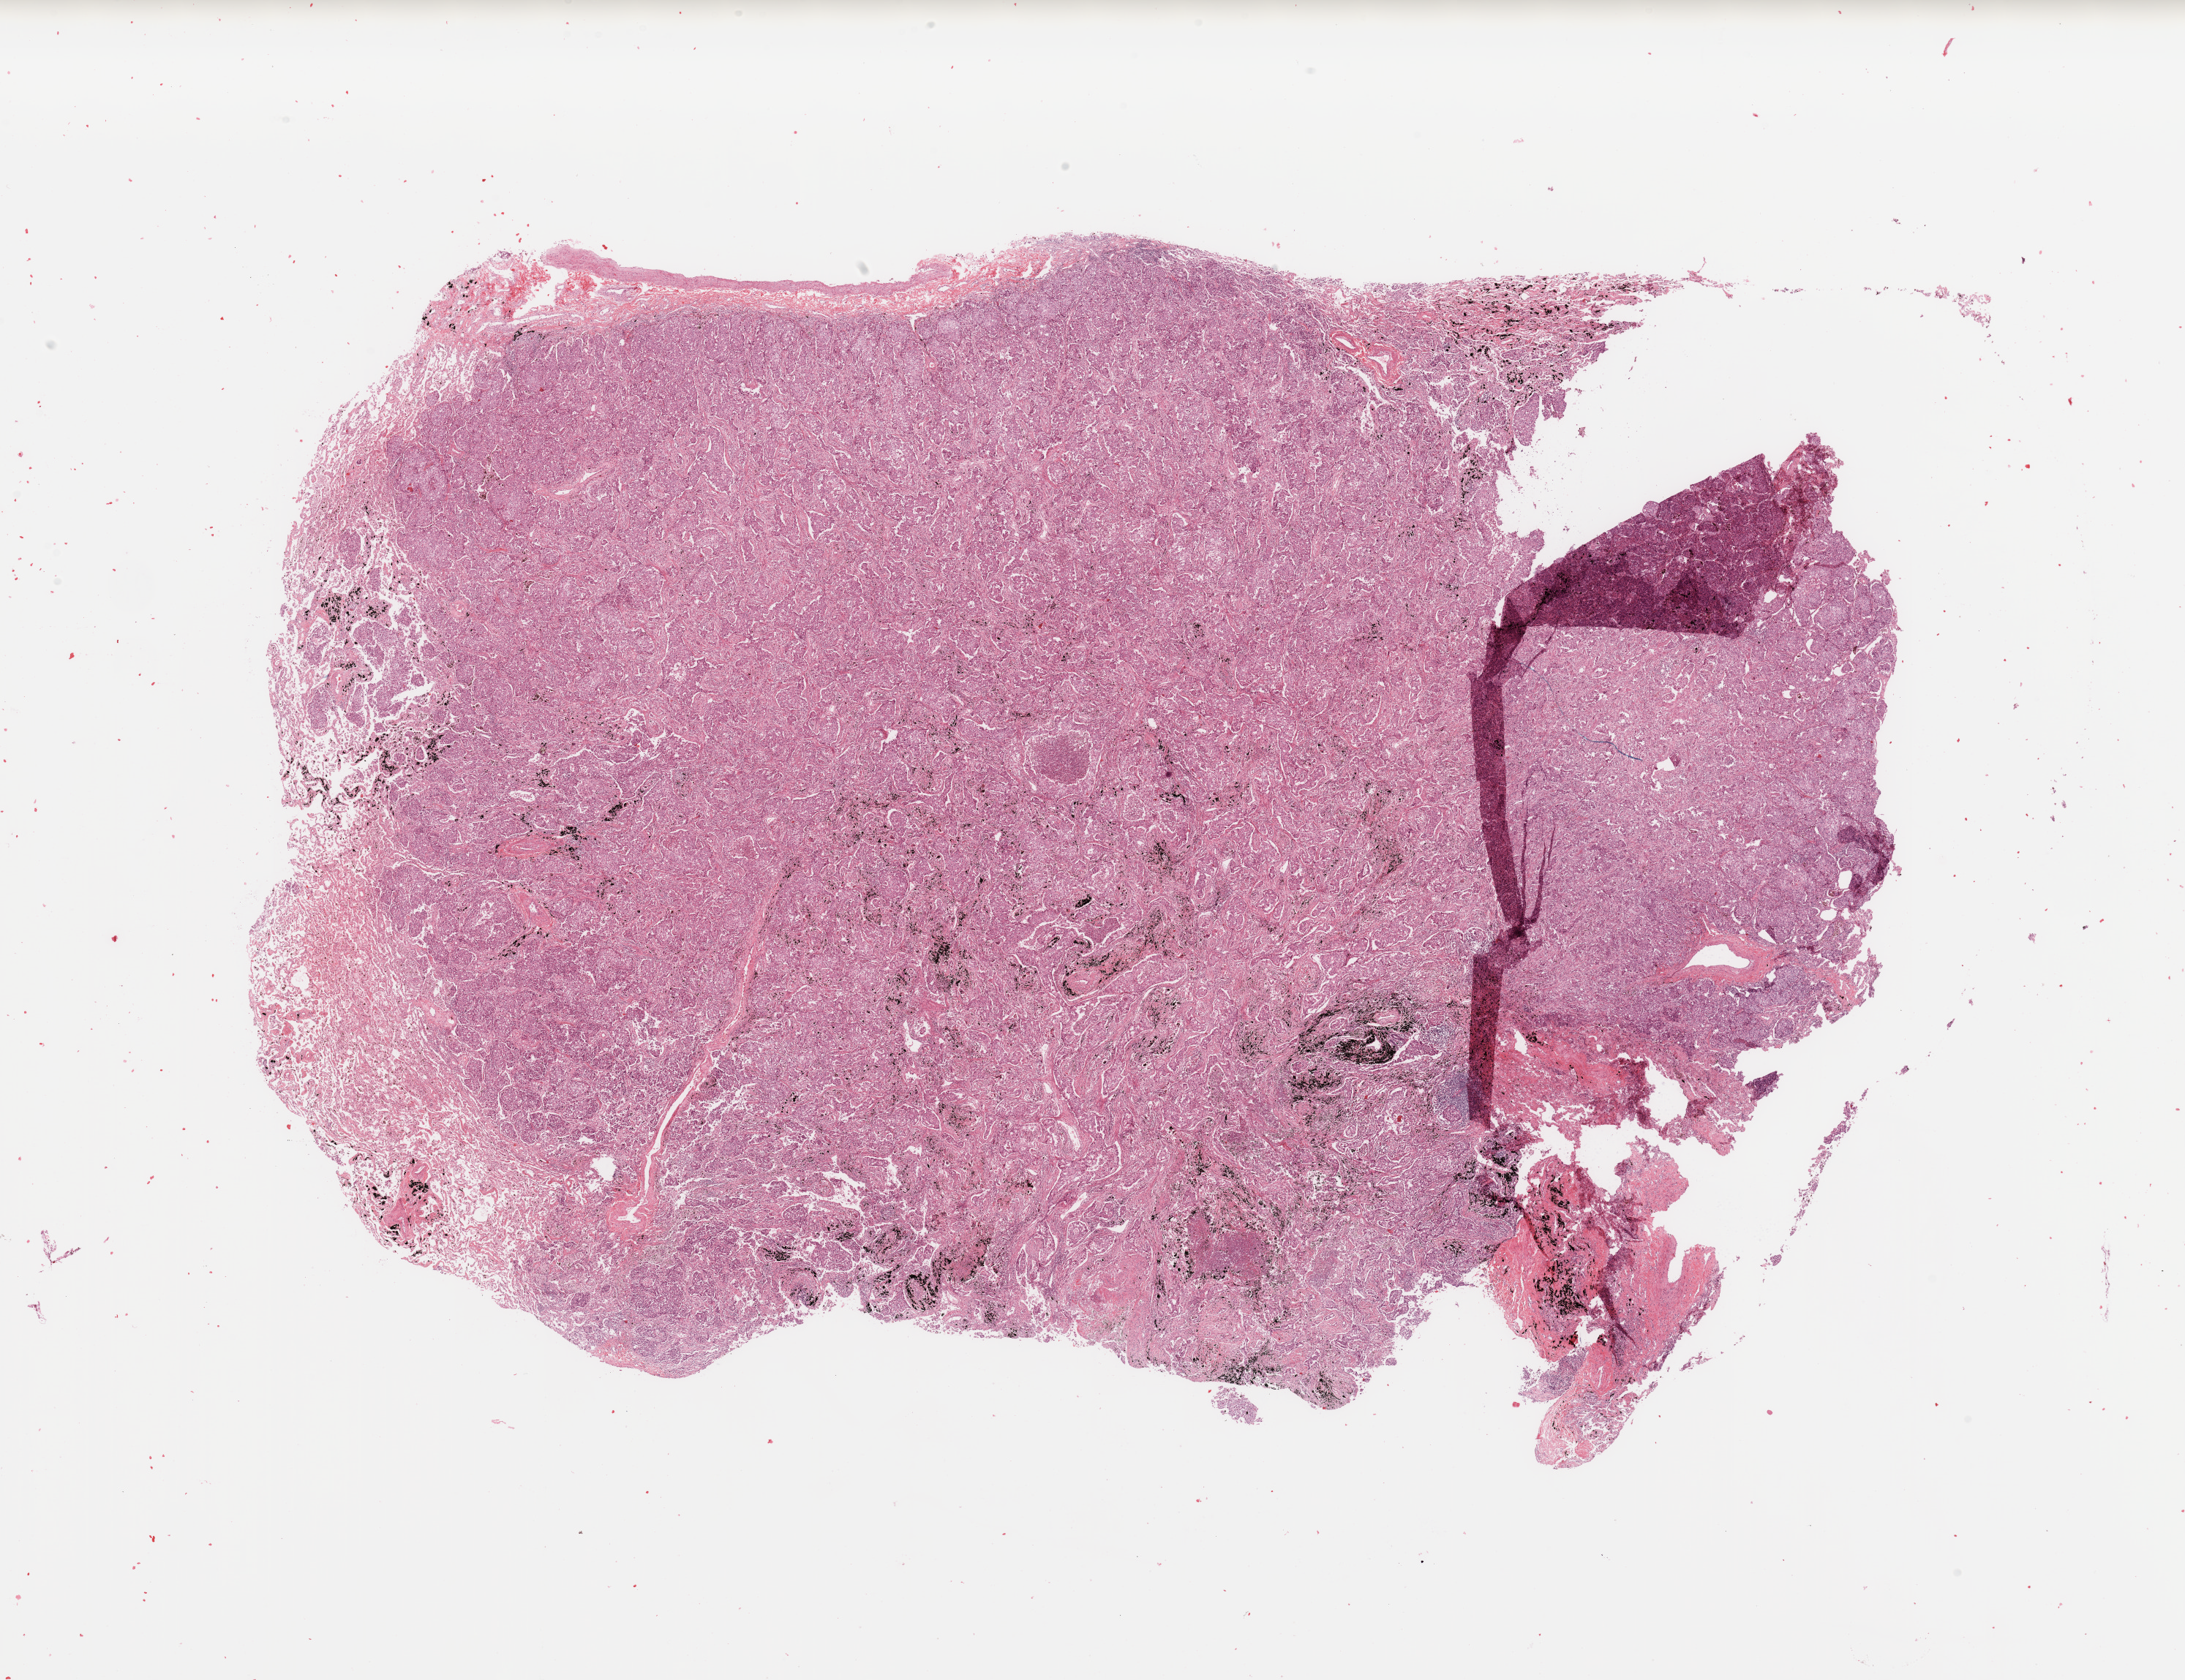
Digitized H&E tissue section (whole slide), whole scanned area (about 23.6 x 18.2 mm, slide scanned at 20x) shown as a low-resolution overview. Lung, tumour tissue. Patient: male, age 54 years. Histologic grade: G3 (poorly differentiated).
• AJCC pathologic stage: IB
• histologic diagnosis: Adenocarcinoma, NOS